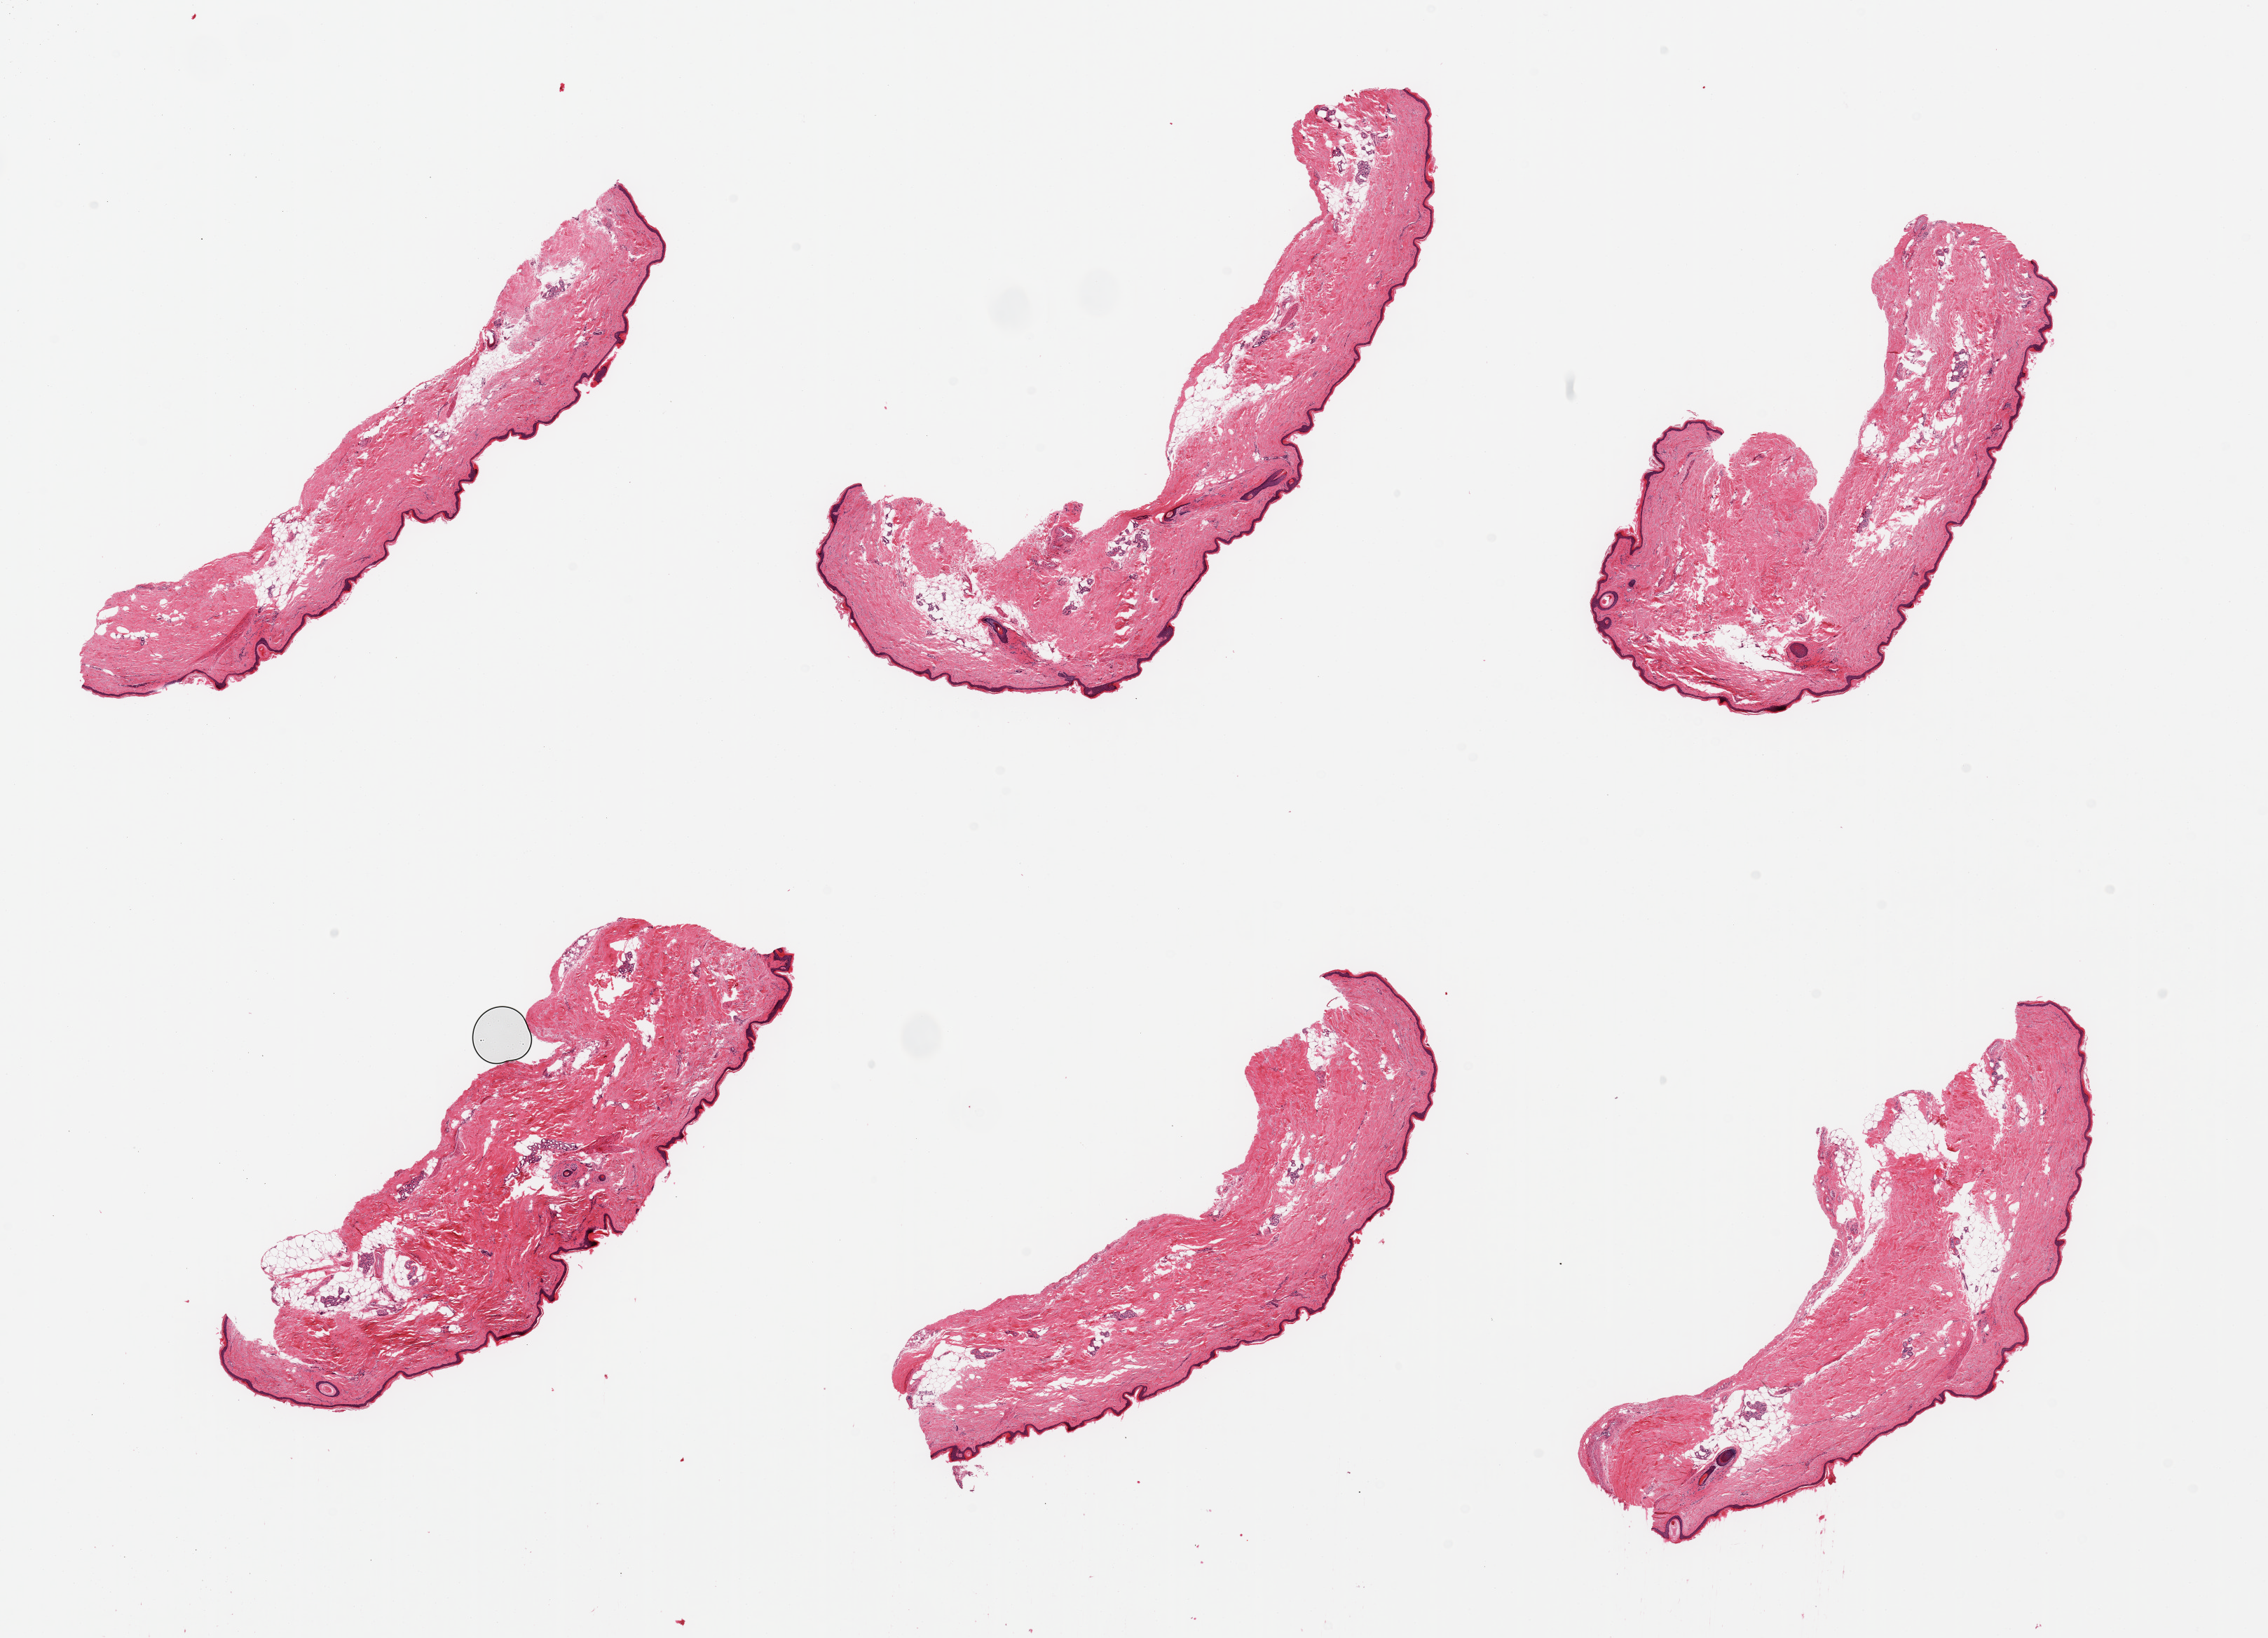
Digitized hematoxylin and eosin (H&E)-stained section, low-resolution overview of the scanned area, about 25.6 x 18.5 mm (acquisition: 20x scan); PAXgene-fixed paraffin-embedded (PFPE) section; section of skin of lower leg (target tissue); tissue donor sample. Female donor.
- reviewer comment on this tissue sample: 6 pieces; 10% dermal fat; well trimmed